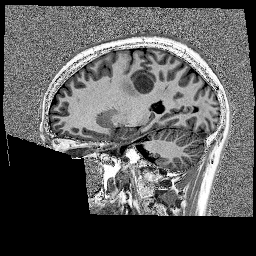
Brain MRI from a brain-tumour surgery series, one sagittal slice. Position 69 of 176 along the scan axis. 256 × 256 image matrix. From the clinical record (not read from this slice): histopathology: Glioblastoma; WHO grade: 4; IDH mutation: no; tumour location: Left Frontal.
Outlined on this slice (expert manual segmentation):
- tumour: bounding box <144,63,169,89> (left, top, right, bottom; pixels)